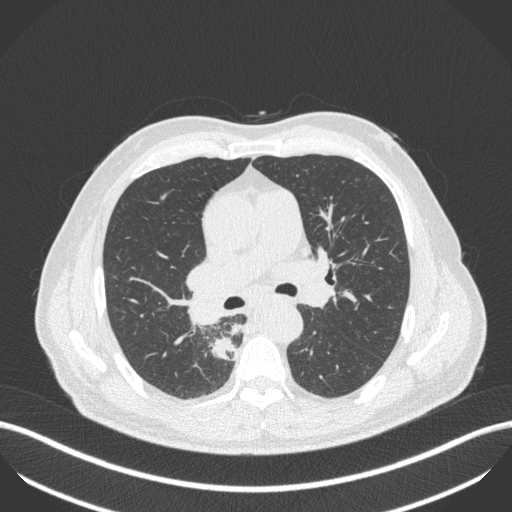
Chest CT, one axial slice. Slice 278 of 451 in the series (ordered by position). 100 kVp. Lung window (W 1500 / L -600 HU). 1 mm slice thickness. 512 × 512 image matrix. Male patient, age 61 years. Case-level facts recorded for this patient, not image findings: clinical TNM (as recorded): T1 N0 M0.
Outlined on this slice (rectangle marked by the reading radiologist):
- lung tumour (recorded histology: small cell carcinoma): bounding box [x1, y1, x2, y2] px = [205, 337, 241, 364]